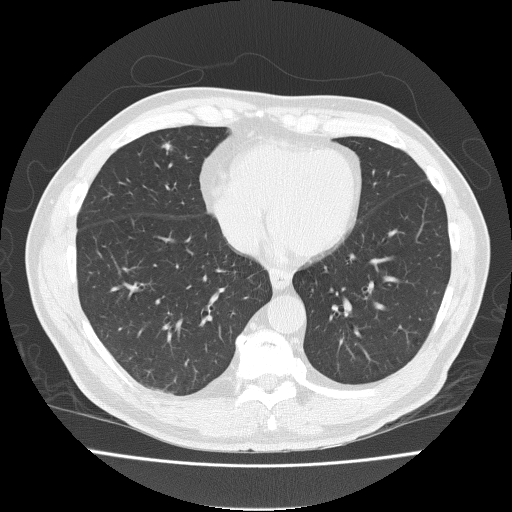
Chest CT (low-dose screening protocol), one axial image, first (baseline) screen, lung window (W 1500 / L -600 HU), slice 127 of 191 in the series, 512 × 512 image matrix. Male, age 57 years at enrolment. Current smoker at enrolment.
- Expert reader's lesion annotation, bounding box (x1, y1, x2, y2) in pixels: (153, 134, 184, 165).
- Reader record for this screening exam (exam-level; its link to the box is not recorded): non-calcified nodule or mass ≥4 mm, right middle lobe, 4 × 4 mm, spiculated (stellate) margins, soft tissue attenuation.
- Official screen result: positive, change unspecified: nodule(s) >= 4 mm or enlarging nodule(s), mass(es), or other non-specific abnormalities suspicious for lung cancer.